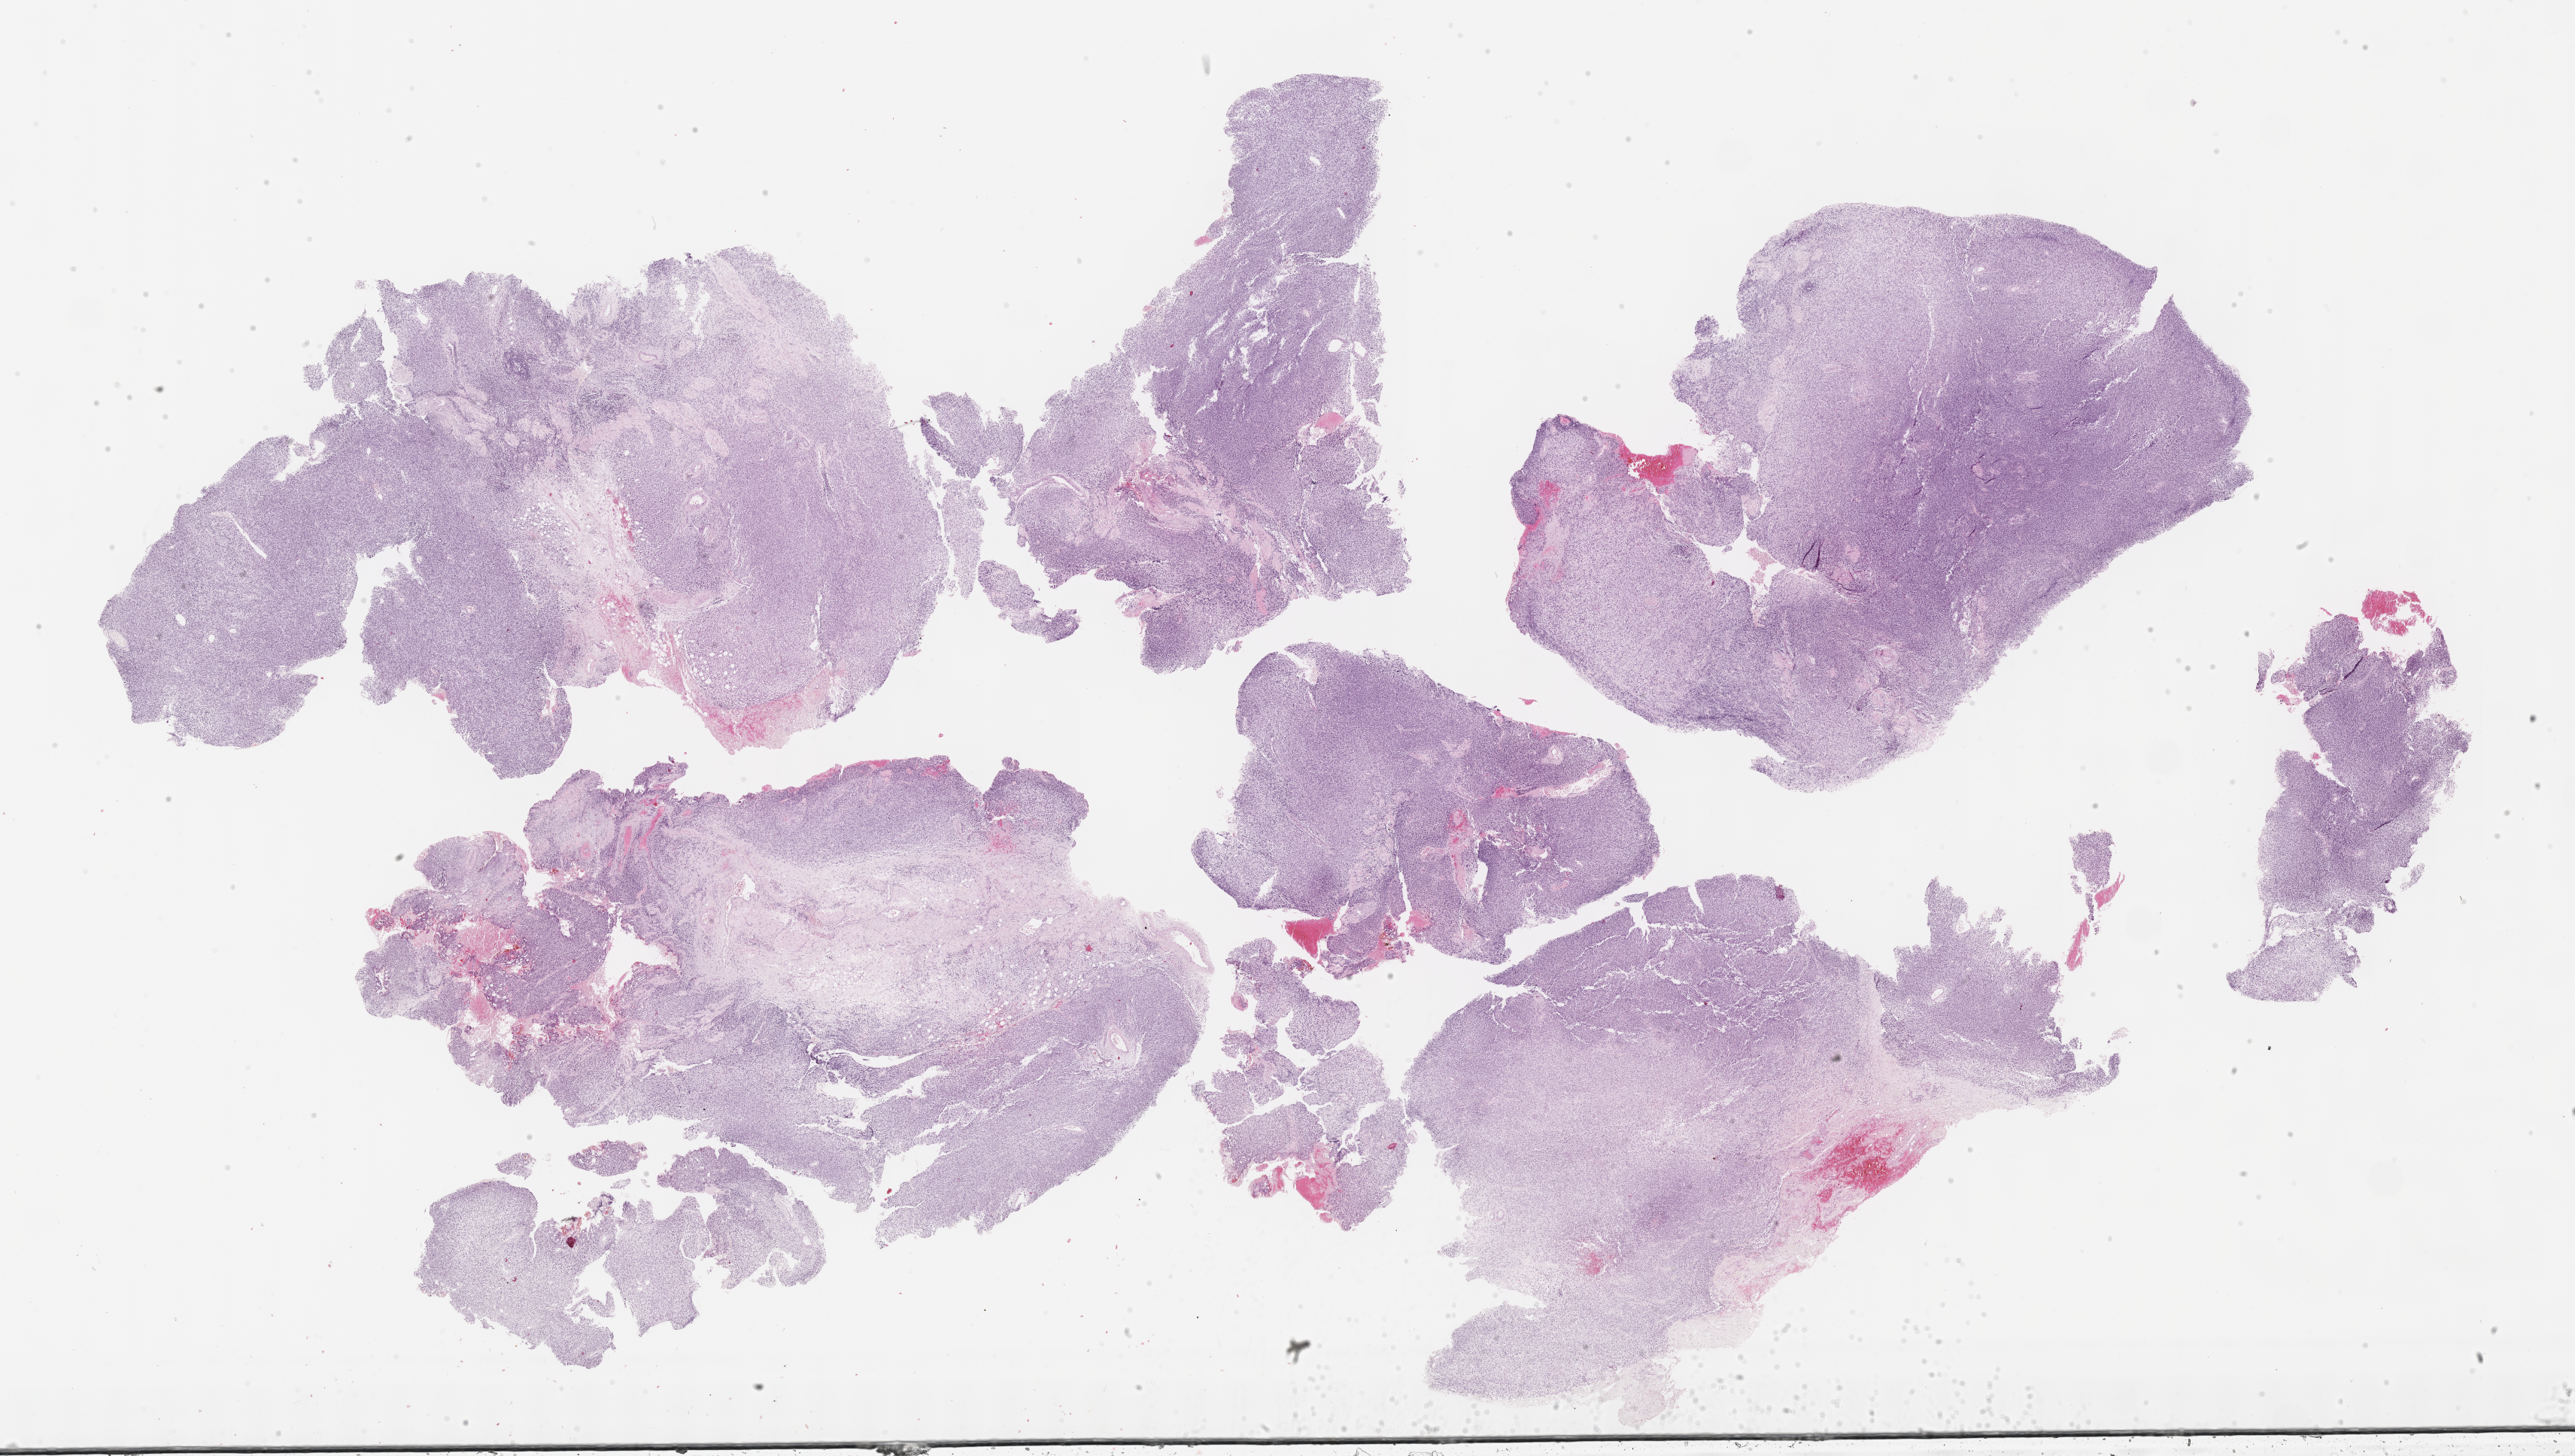
H&E whole-slide image of tumor tissue, whole scanned area (about 27.7 x 15.7 mm) shown as a low-resolution overview, FFPE section, sample anatomic site: eye, orbit-left anterior. Patient: male, age 13.4 years at diagnosis.
• metastatic status at presentation (as recorded): non-metastatic
• stage (as recorded): 1
• diagnosis: rhabdomyosarcoma; histological classification: embryonal rhabdomyosarcoma